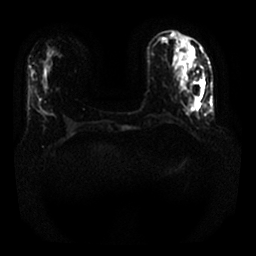
Breast MRI, one axial slice. Slice 4 of 25 in the series (ordered by position). Diffusion-weighted series; image 2 of 4 stored at this slice position (different b-values; order by instance number). 1.5 T. 4 mm slice thickness. 256 × 256 image matrix, field of view 340 × 340 mm. Female patient.
Structures marked on this image (manually delineated by an expert):
- tumour on diffusion-weighted imaging: bounding box [x1, y1, x2, y2] px = [193, 83, 204, 104]